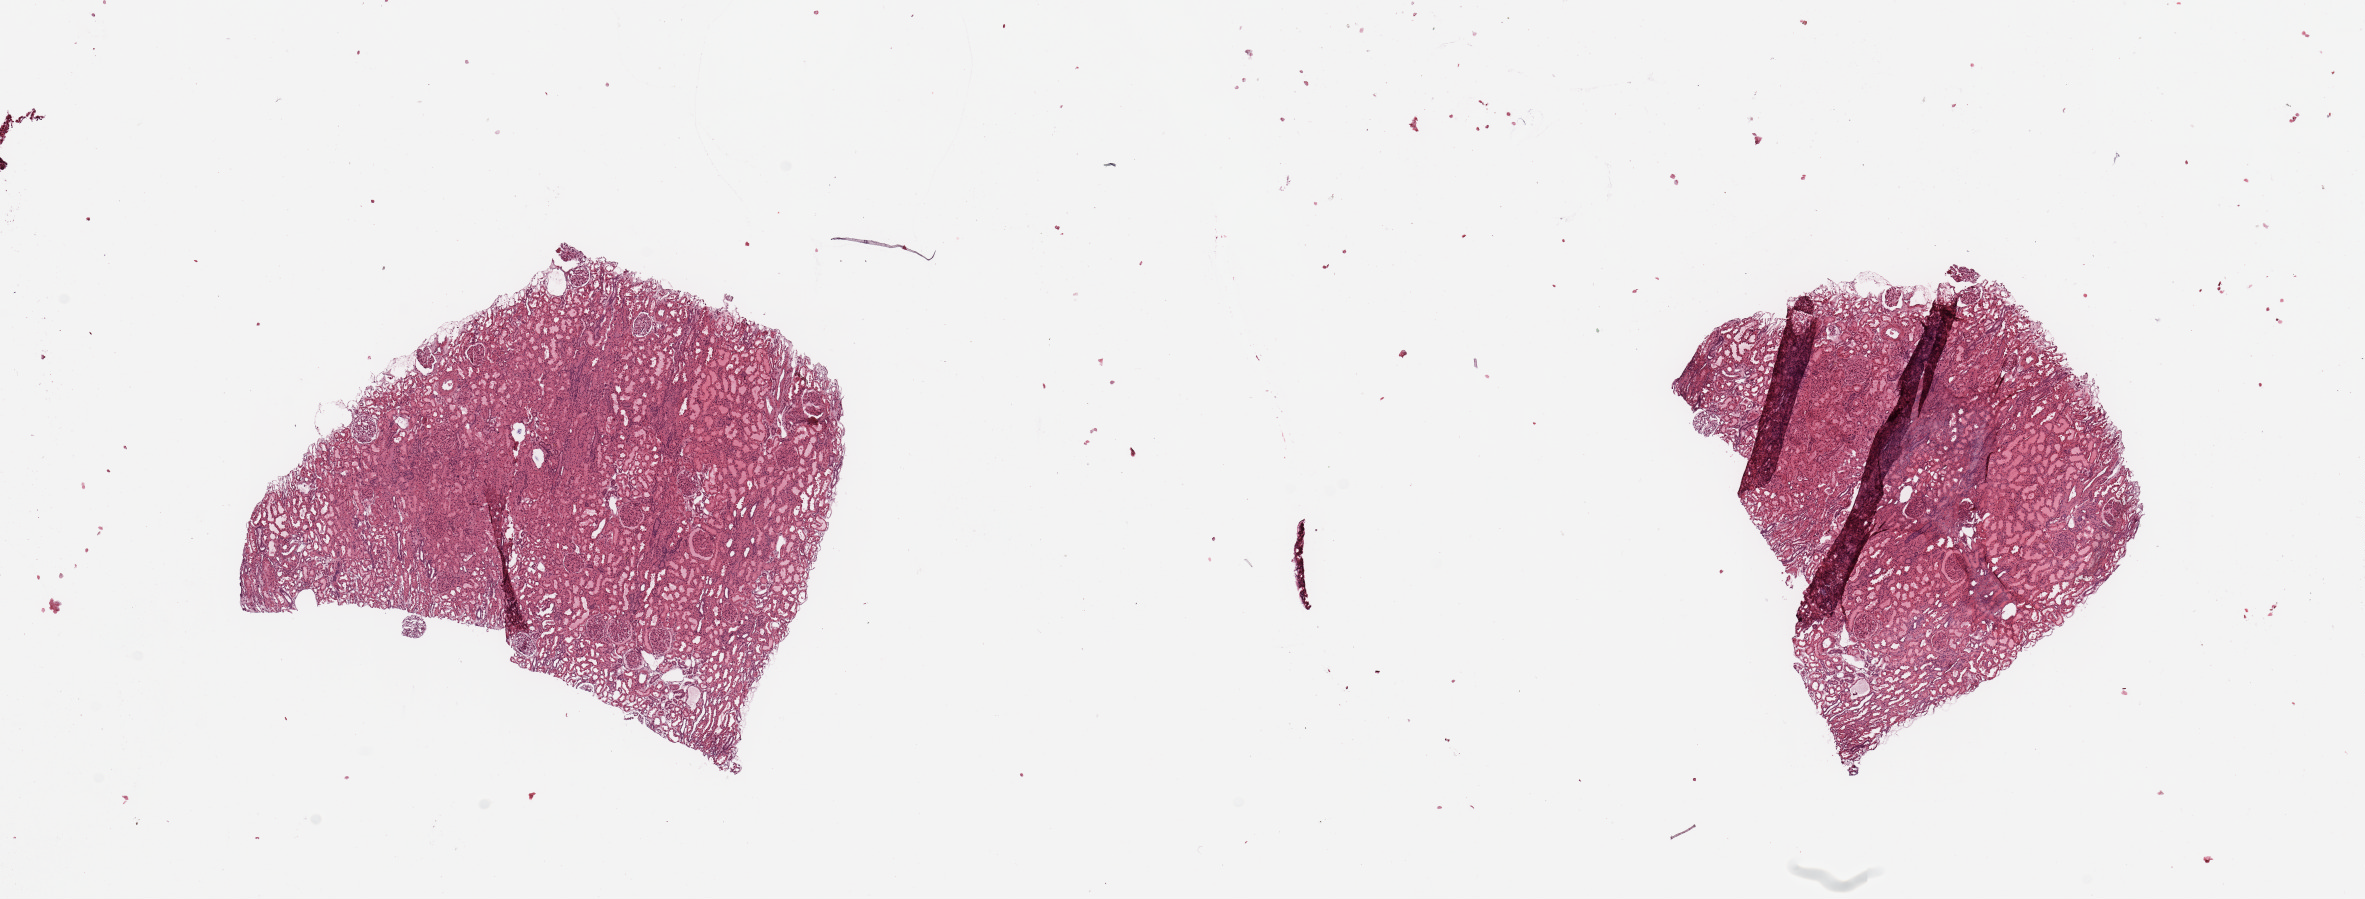
Digitized H&E-stained tissue section (whole slide) — whole scanned area (about 18.7 x 7.1 mm) shown as a low-resolution overview, normal (non-tumour) tissue sample, sampled site: kidney. Male, 59 y/o.
* this section: normal (non-tumour) tissue from the same patient
* patient diagnosis: Renal cell carcinoma, NOS